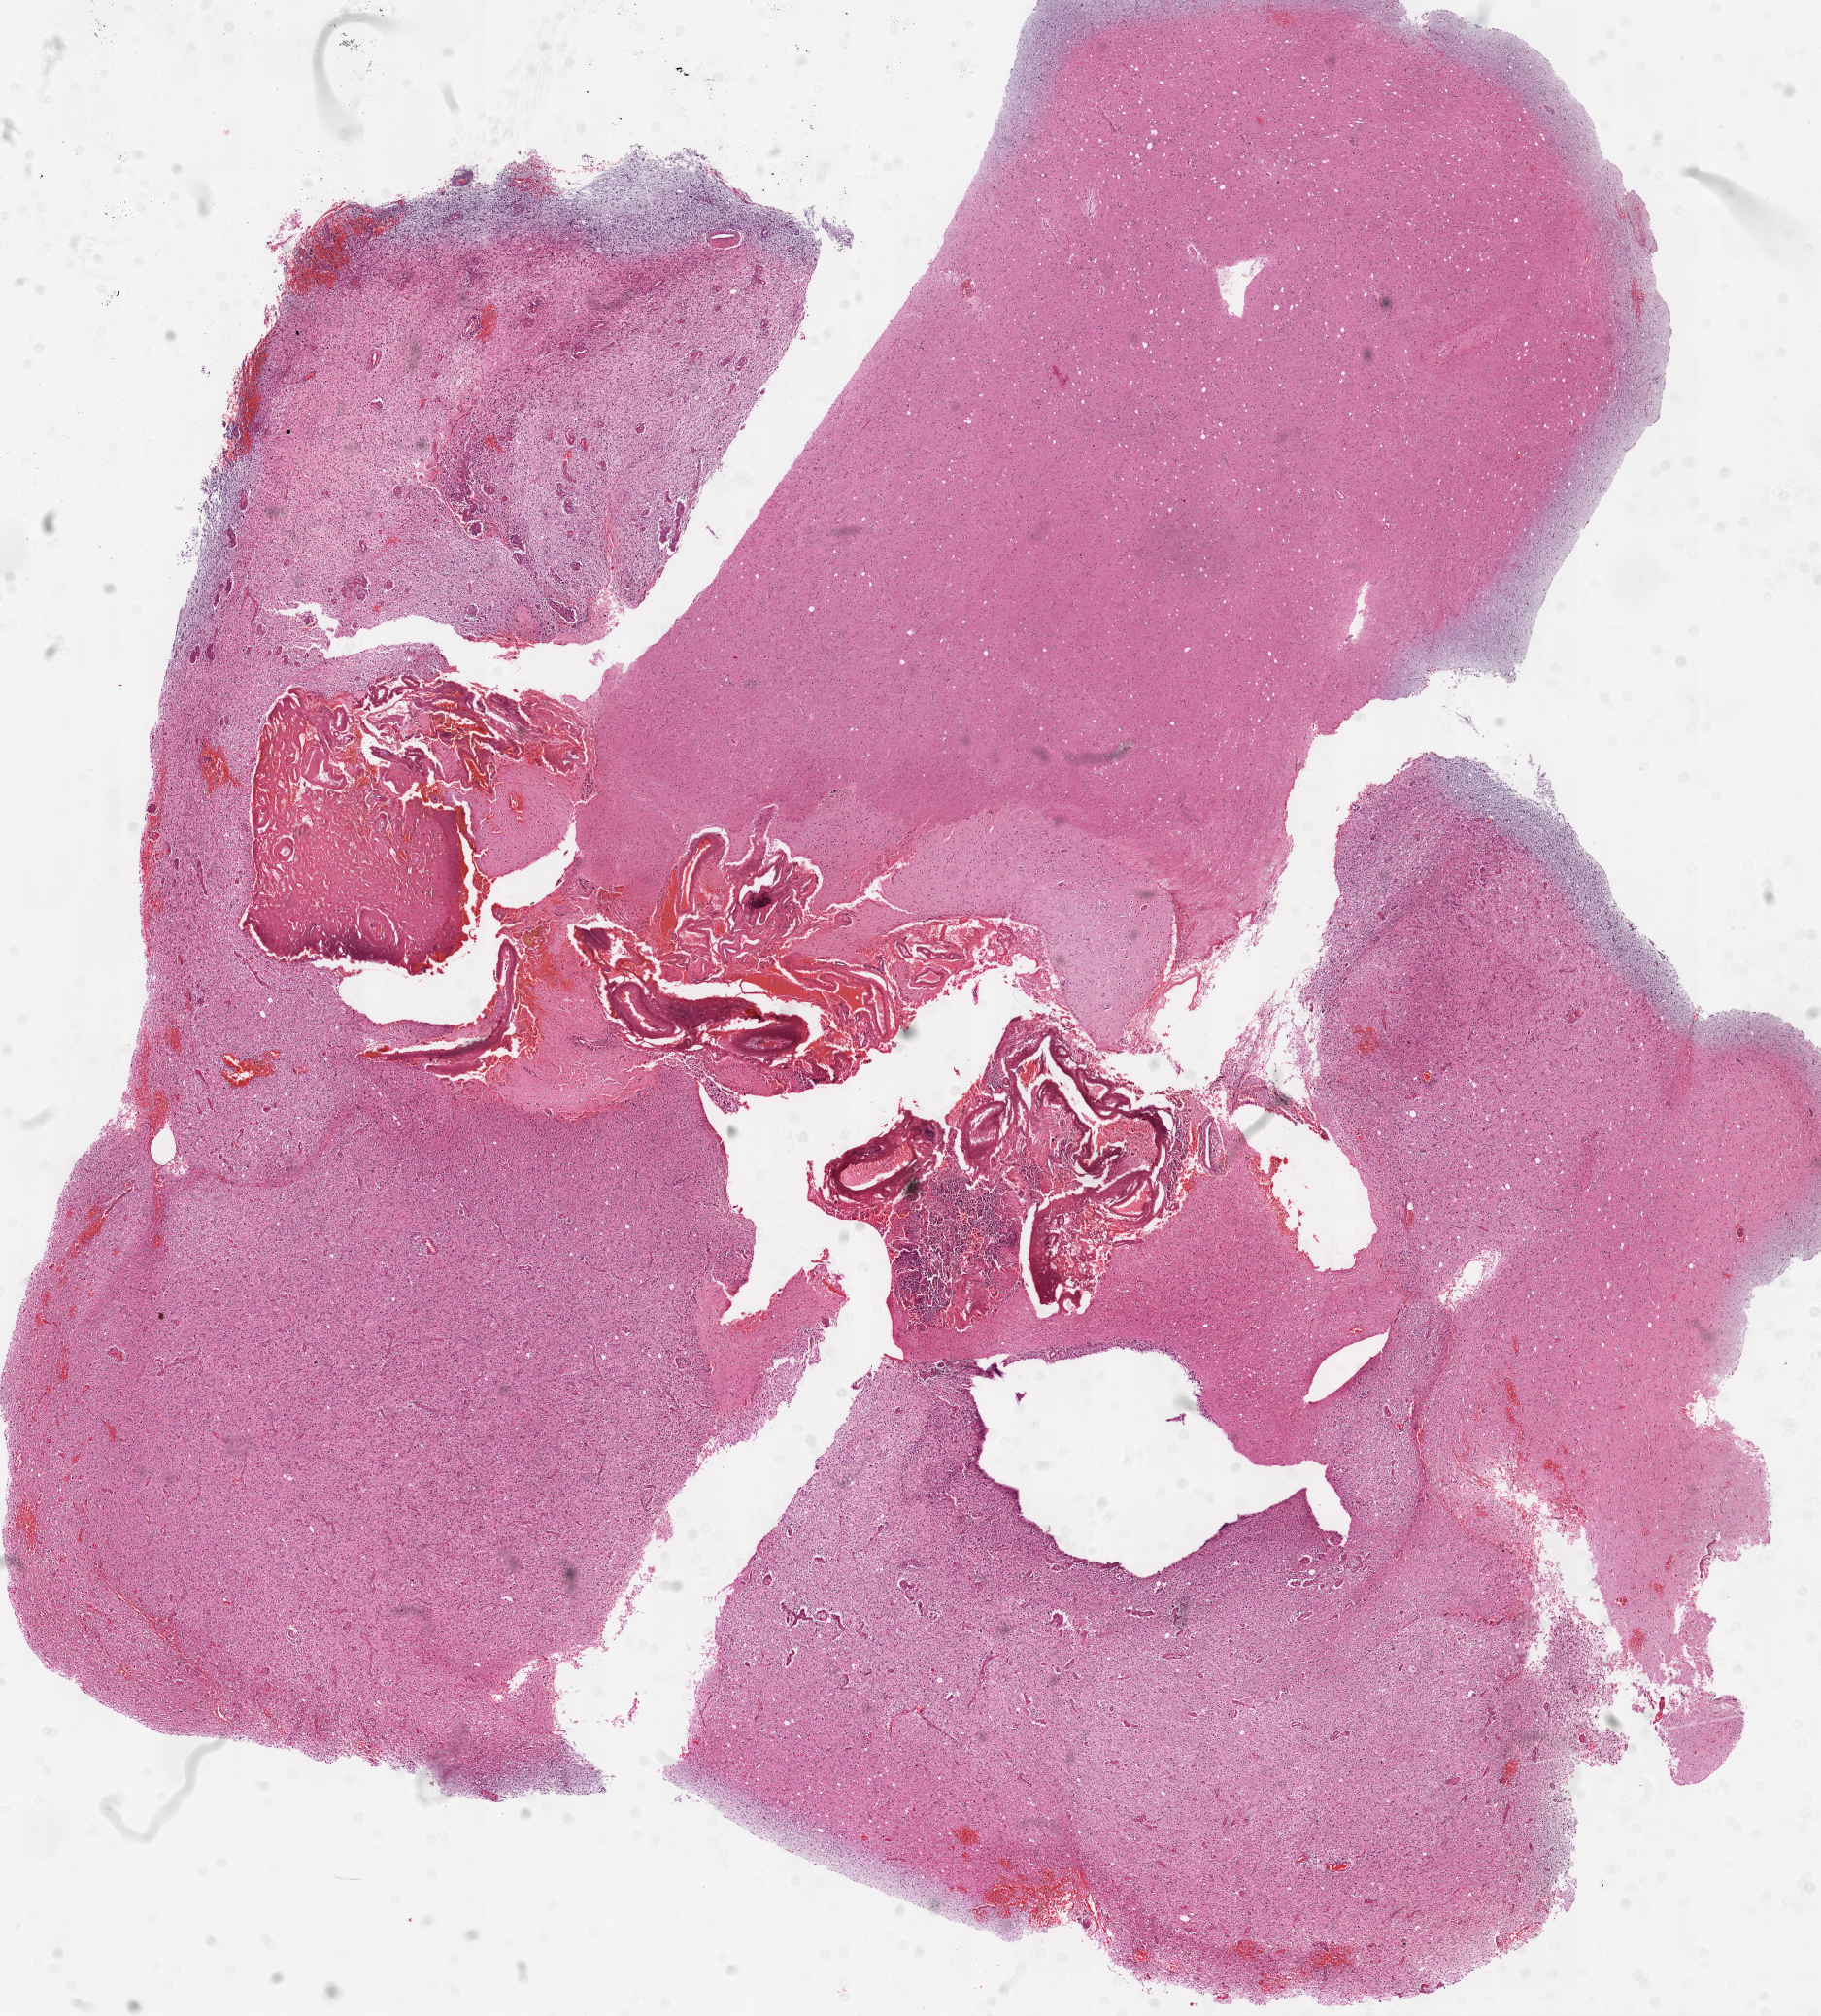
Whole-slide histology image, H&E-stained, shown as a low-resolution overview of the whole scanned area (about 15.0 x 16.7 mm), FFPE section, sample: primary tumour, brain. Male, age 67 years at initial diagnosis.
Diagnosis: Glioblastoma.